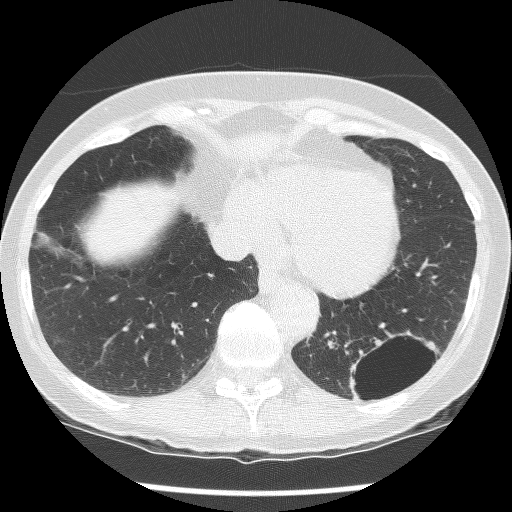
Axial slice from a low-dose chest CT screening exam, second screening round (one year after baseline), lung window (W 1500 / L -600 HU), 2.5 mm slice thickness. Female participant, aged 61 years at enrolment. Current smoker at enrolment.
Expert-annotated lung lesion, box from (x=330, y=320) to (x=438, y=415) px. The screening reader recorded 2 non-calcified nodules or masses ≥4 mm on this exam; which of them this box marks is not recorded. Participant outcome: lung cancer diagnosed 585 days after this screen (after the third annual screen) — non-small cell carcinoma, left lower lobe, poorly differentiated (G3), stage IB (AJCC 6th edition), 100 mm at pathology.